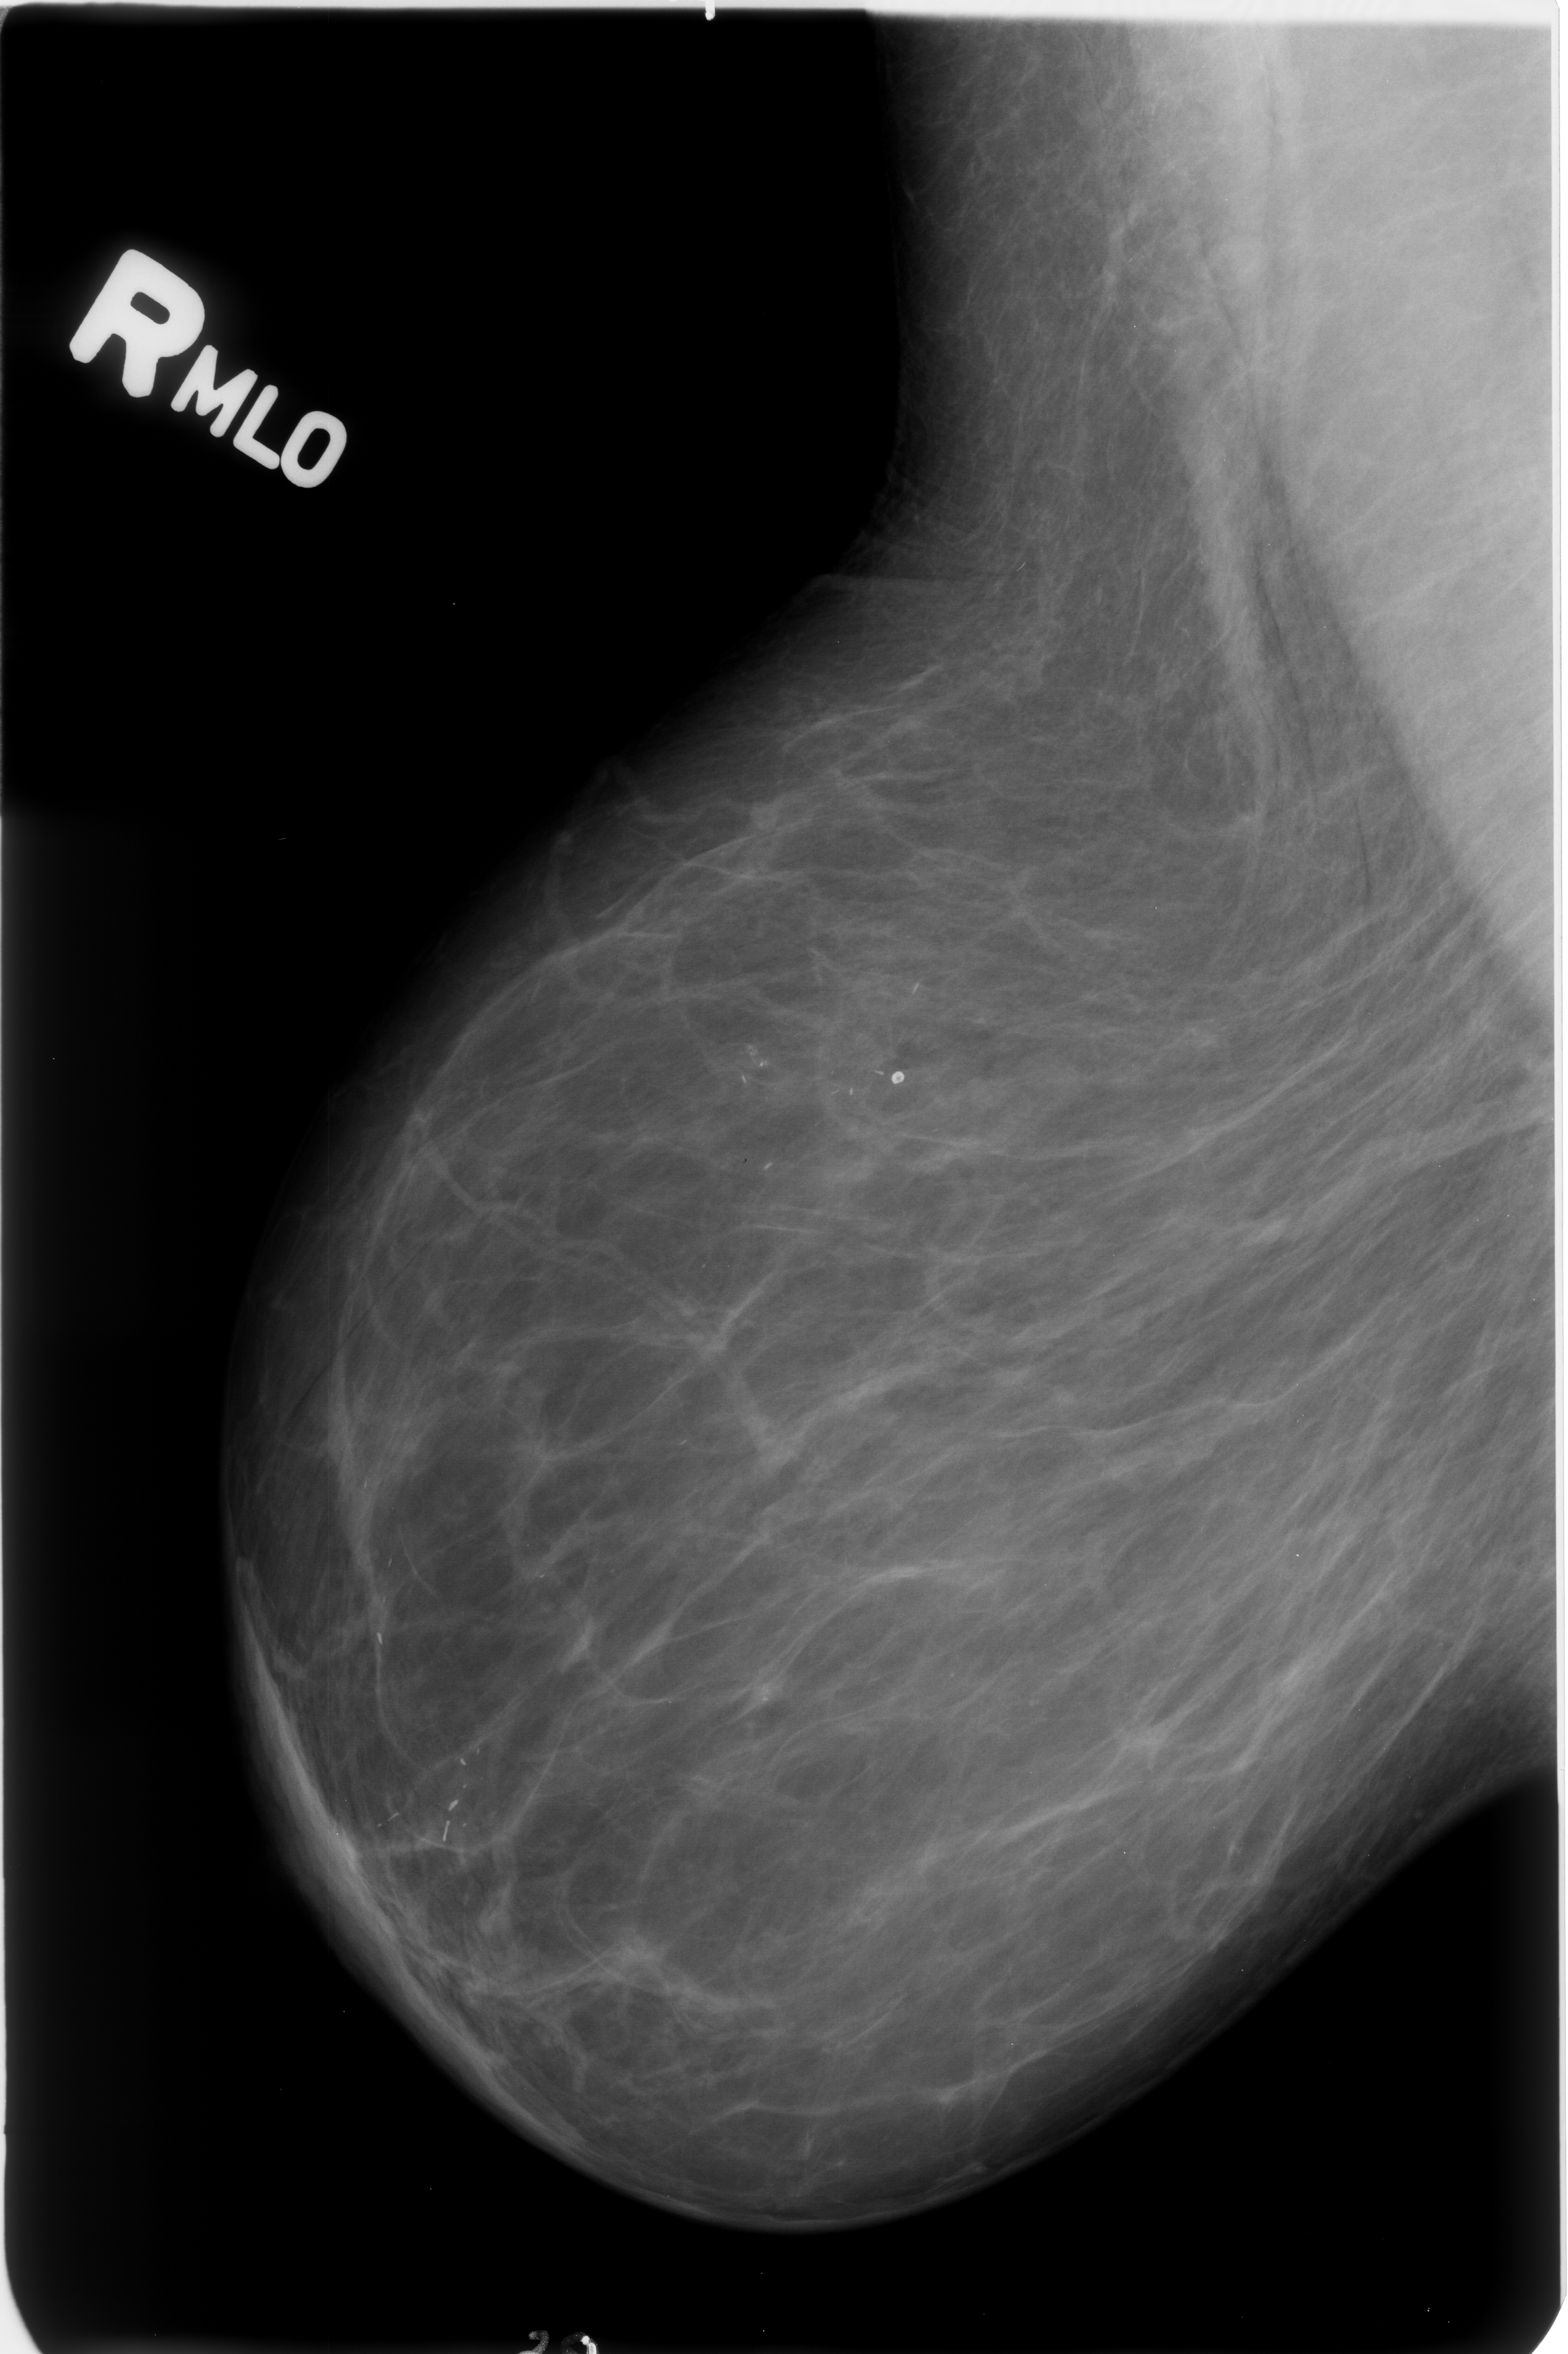
Digitized screen-film mammogram; right breast; mediolateral oblique (MLO) view.
Radiologist-marked abnormalities on this image: Finding 1 of 5: calcifications, distribution regional; BI-RADS assessment category 2; subtlety rating 3 on a 1 (subtle) to 5 (obvious) scale; benign; no additional work-up was recommended (benign without callback). Finding 2 of 5: calcifications, distribution regional; BI-RADS assessment category 2; subtlety rating 3 on a 1 (subtle) to 5 (obvious) scale; benign; no additional work-up was recommended (benign without callback). Finding 3 of 5: calcifications, distribution regional; BI-RADS assessment category 2; benign; no additional work-up was recommended (benign without callback). Finding 4 of 5: calcifications, distribution regional; BI-RADS assessment category 2; subtlety rating 3 on a 1 (subtle) to 5 (obvious) scale; benign without callback (not worked up further). Finding 5 of 5: calcifications, distribution regional; BI-RADS assessment category 2; subtlety rating 3 on a 1 (subtle) to 5 (obvious) scale; benign; no additional work-up was recommended (benign without callback).